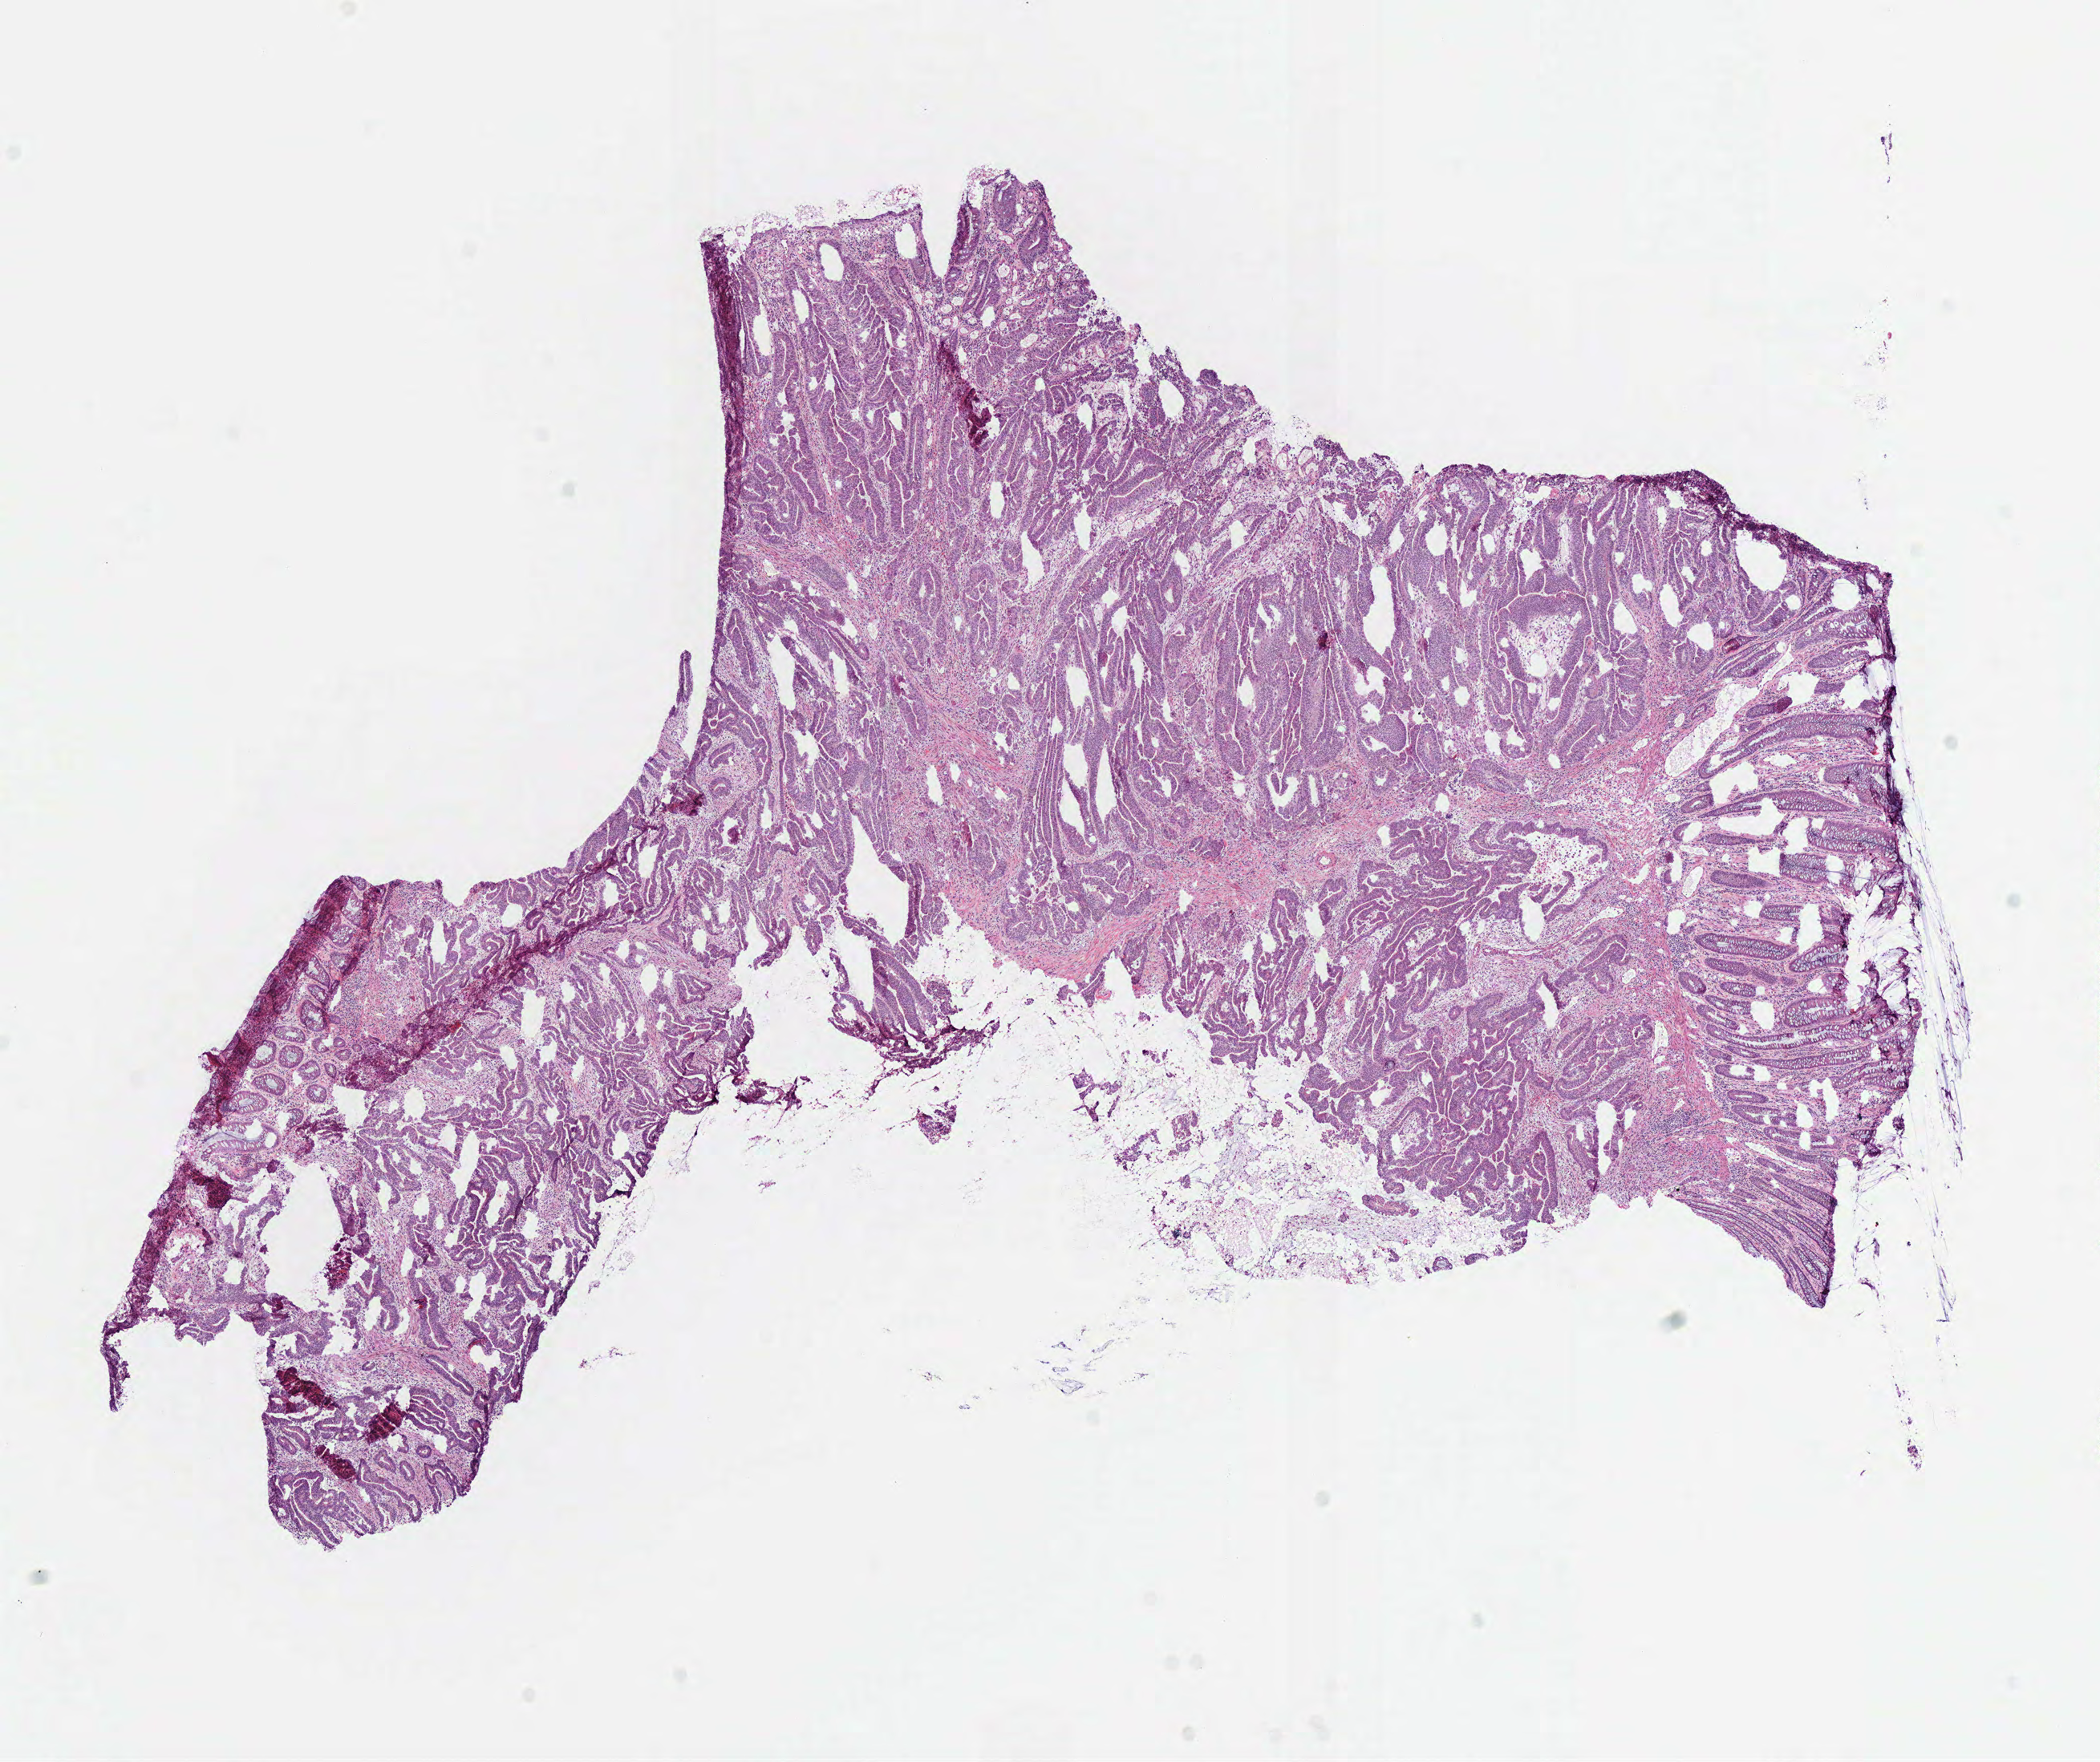
Digitized H&E tissue section (whole slide), whole scanned area (about 10.3 x 8.7 mm) shown as a low-resolution overview, frozen section, sample: primary tumour, rectum. Male, age 71 years at initial diagnosis. Pathologist review of this section (percent, as recorded): tumour cells 76%, tumour nuclei 73%, normal cells 12%, stromal cells 12%, necrosis 0%.
• TNM: T3 N1 M0
• AJCC pathologic stage: IIIA (7th edition)
• lymph nodes positive (case pathology): 3 of 8 examined
• pathologic diagnosis: Tubular adenocarcinoma